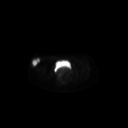
FDG PET of an extremity soft-tissue mass (from a PET/CT study), one axial slice. Slice 67 of 267 in the series (ordered by position). 3.27 mm slice thickness. 128 × 128 image matrix, field of view 700 × 700 mm. Patient: female, 34 years. From the clinical record (not read from this slice): histological type: synovial sarcoma; grade: intermediate; site of the primary tumour: right thigh.
Annotated regions visible in this slice (expert contour drawn on MRI and transferred to this co-registered scan by the dataset authors):
- gross tumour volume including surrounding oedema: bounding box <31,57,40,68> (left, top, right, bottom; pixels)
- gross tumour volume (mass): <31,57,40,67>